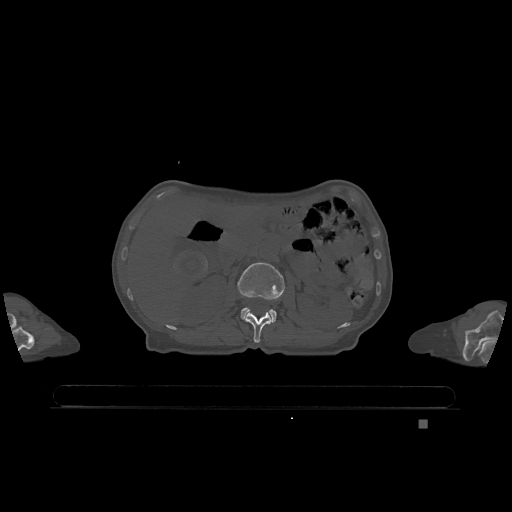
CT including the spine, one axial slice; position 446 of 1317 along the scan axis; bone window (W 1800 / L 400 HU); 0.5 mm slice thickness; 512 × 512 image matrix, field of view 500 × 500 mm. Patient: female, 74 years. From the clinical record (not read from this slice): primary cancer: lung; vertebrae with lytic lesions (as recorded): T1, T4, T5, T6, L4, L5.
Structures marked on this image (semi-automatically segmented with operator editing):
- L1 vertebra: bounding box (x1, y1, x2, y2) in pixels: (244, 312, 272, 343)
- L2 vertebra: (238, 262, 285, 323)